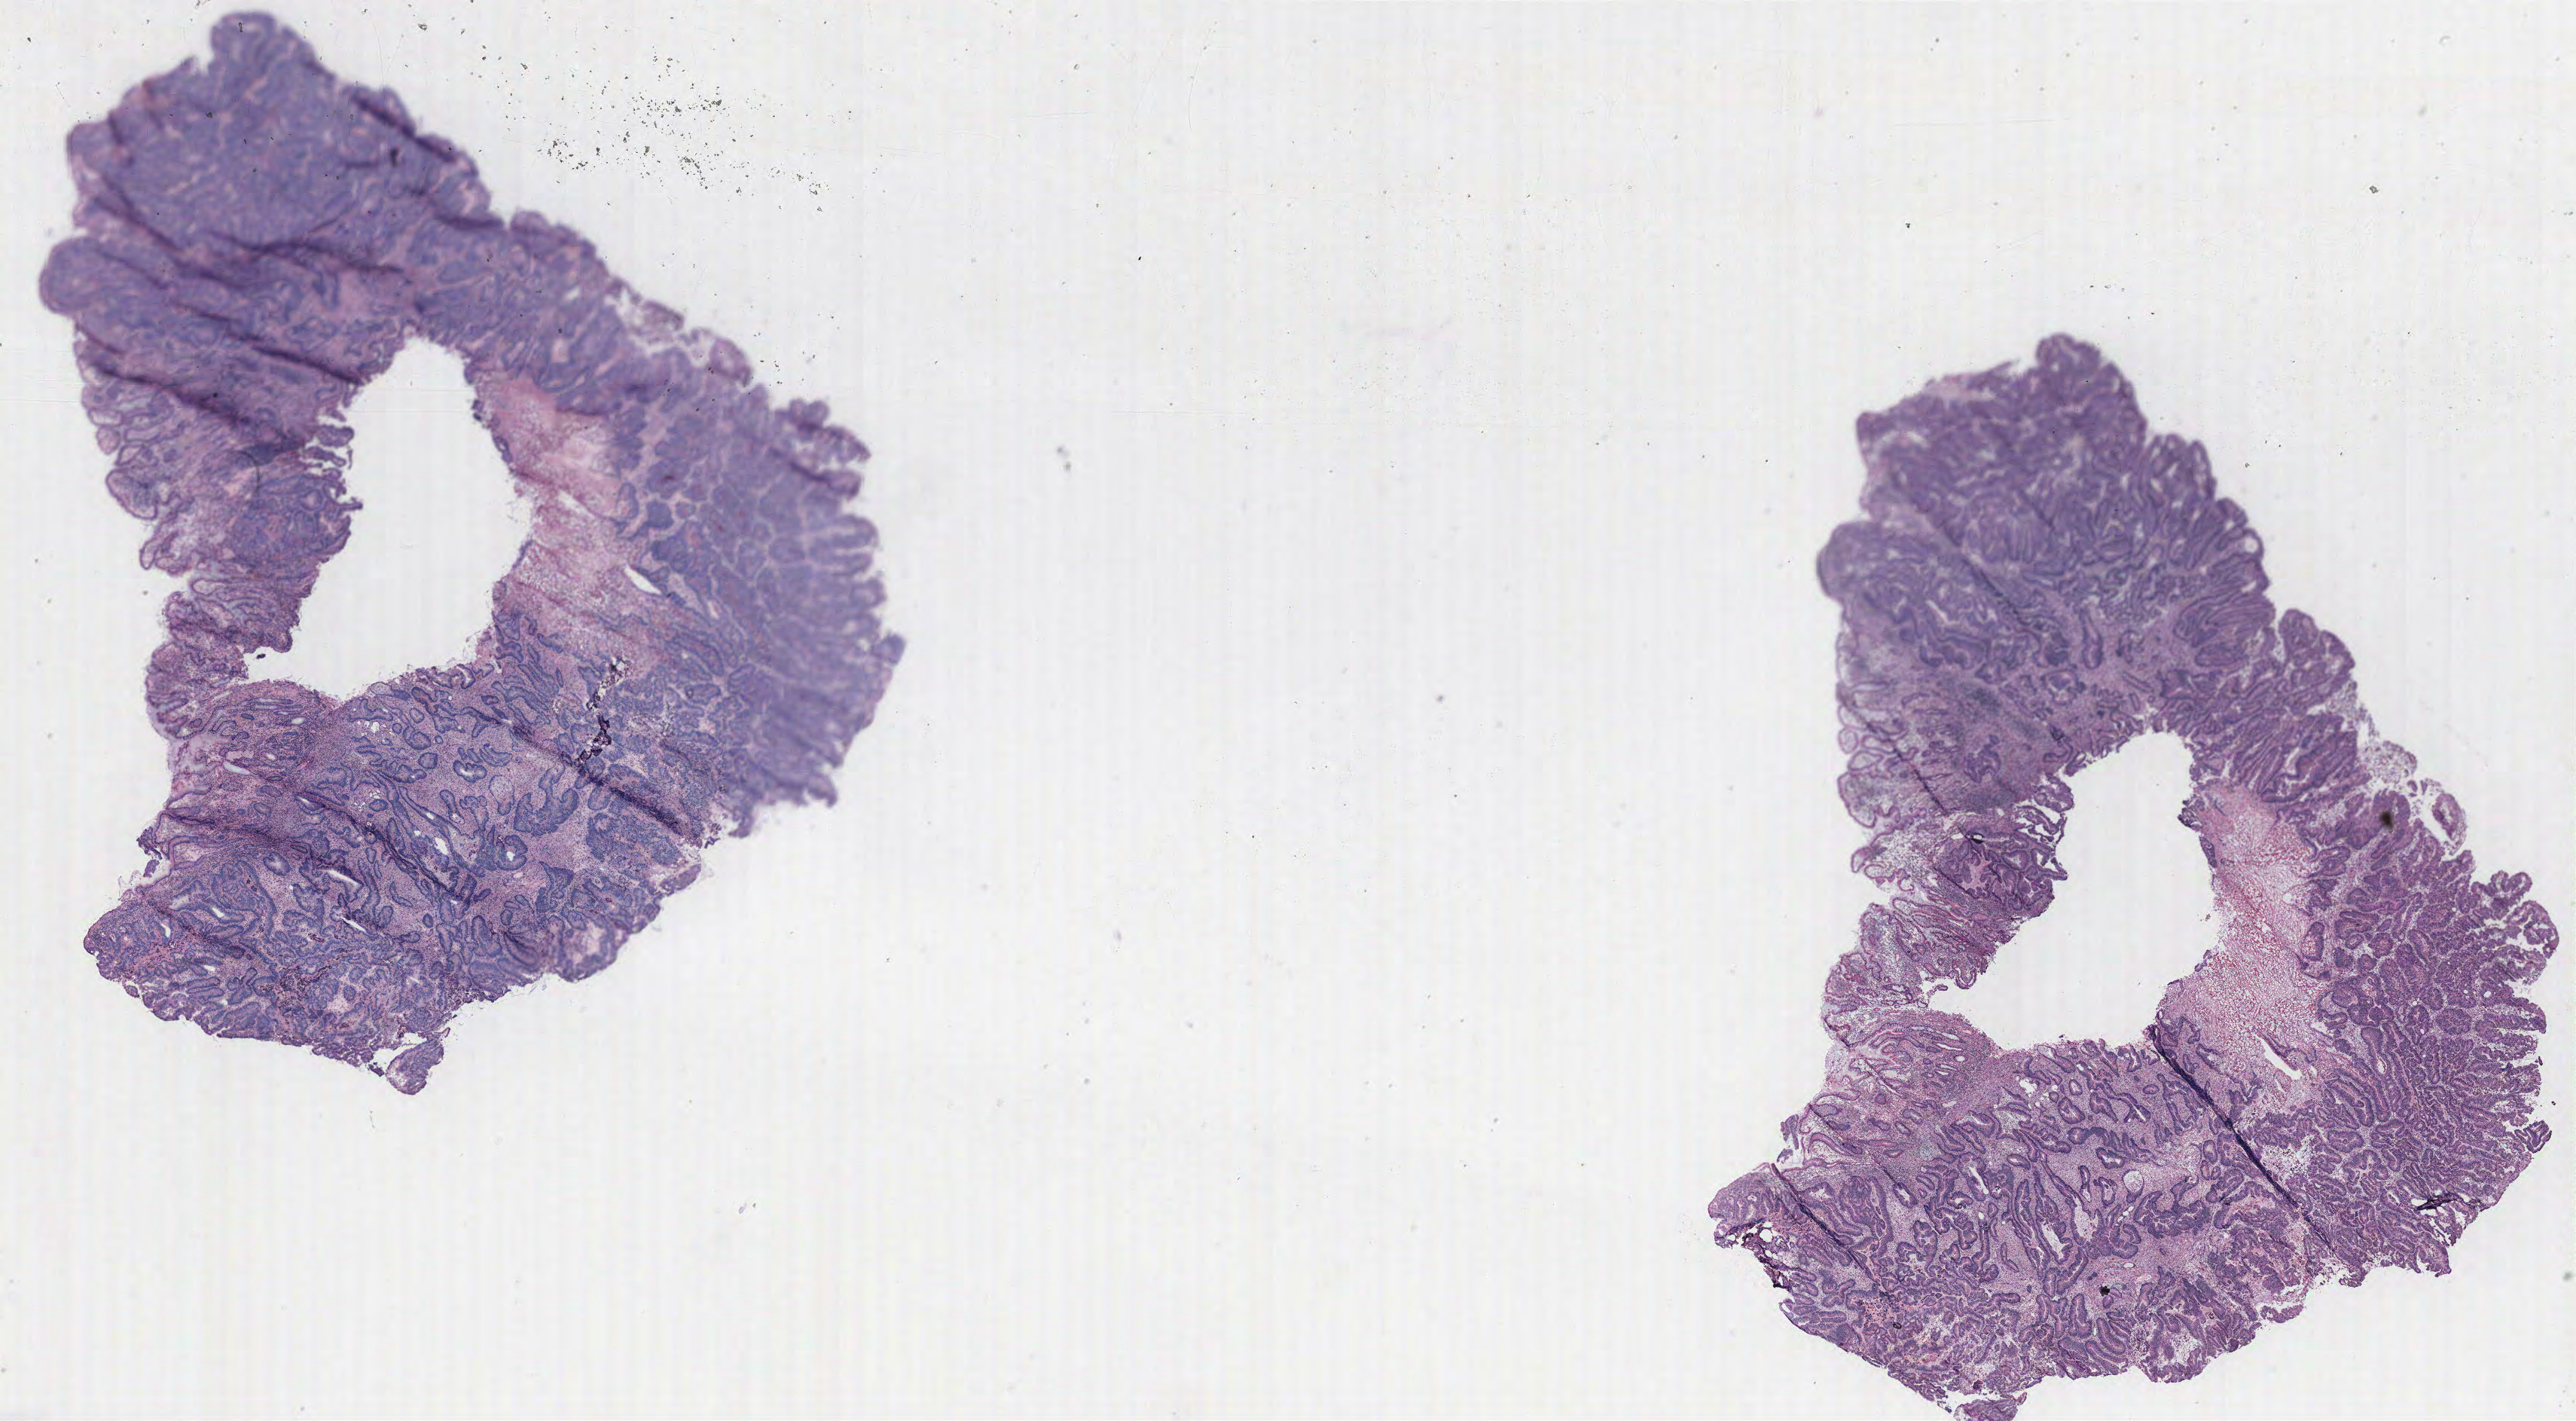
Whole-slide histology image, Hematoxylin and eosin (H&E) stained, shown as a low-resolution overview of the whole scanned area (about 27.4 x 15.1 mm, slide scanned at 40x); colon, tissue type not recorded.
Patient diagnosis (cohort enrolment): colon cancer (colon).